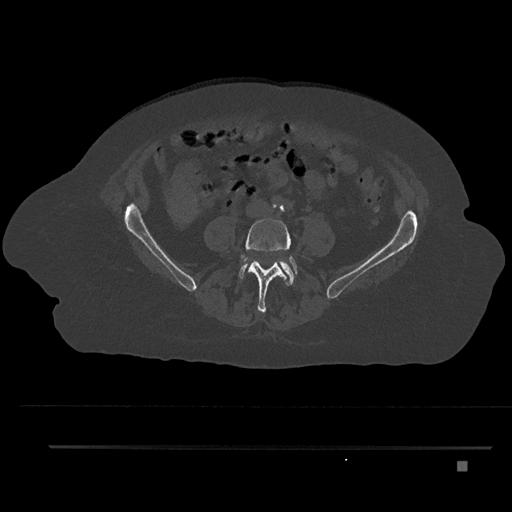
CT including the spine, one axial slice; slice 74 of 797 in the series (ordered by position); reconstruction kernel Br40s/3; 120 kVp; bone window (W 1800 / L 400 HU); 0.5 mm slice thickness; 512 × 512 image matrix, field of view 437 × 437 mm. Patient: female, 76 years. Case-level facts recorded for this patient, not image findings: primary cancer: lung; vertebrae with lytic lesions (as recorded): T11, L3.
Annotated regions visible in this slice (semi-automatic segmentation, software-assisted and operator-edited):
- L4 vertebra: bounding box [x1, y1, x2, y2] px = [240, 218, 298, 313]
- L5 vertebra: [239, 259, 297, 285]